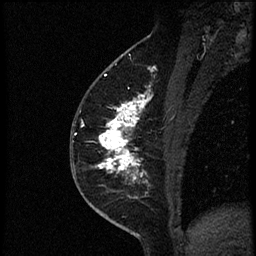
Breast MRI (dynamic contrast-enhanced), one sagittal slice; slice 30 of 56 in the series (ordered by position); dynamic contrast-enhanced study with each time point stored as its own series, time point 2 of 4 at this slice position (early post-contrast, ordered by acquisition time); 1.5 T; TE 4.2 ms, TR 18.9 ms; 256 × 256 image matrix, field of view 200 × 200 mm. Female patient. Case-level facts recorded for this patient, not image findings: setting: breast cancer imaged before/during neoadjuvant chemotherapy; receptor status: HER2-positive.
Annotated regions visible in this slice (semi-automatically segmented with operator editing):
- analysis volume of interest (the breast-tissue region the enhancement analysis was run in; not a lesion): box from (x=78, y=85) to (x=174, y=189) px
- tumour enhancement mask (voxels above the 100 % enhancement threshold inside the analysis volume of interest): (x=83, y=89)–(x=152, y=182)